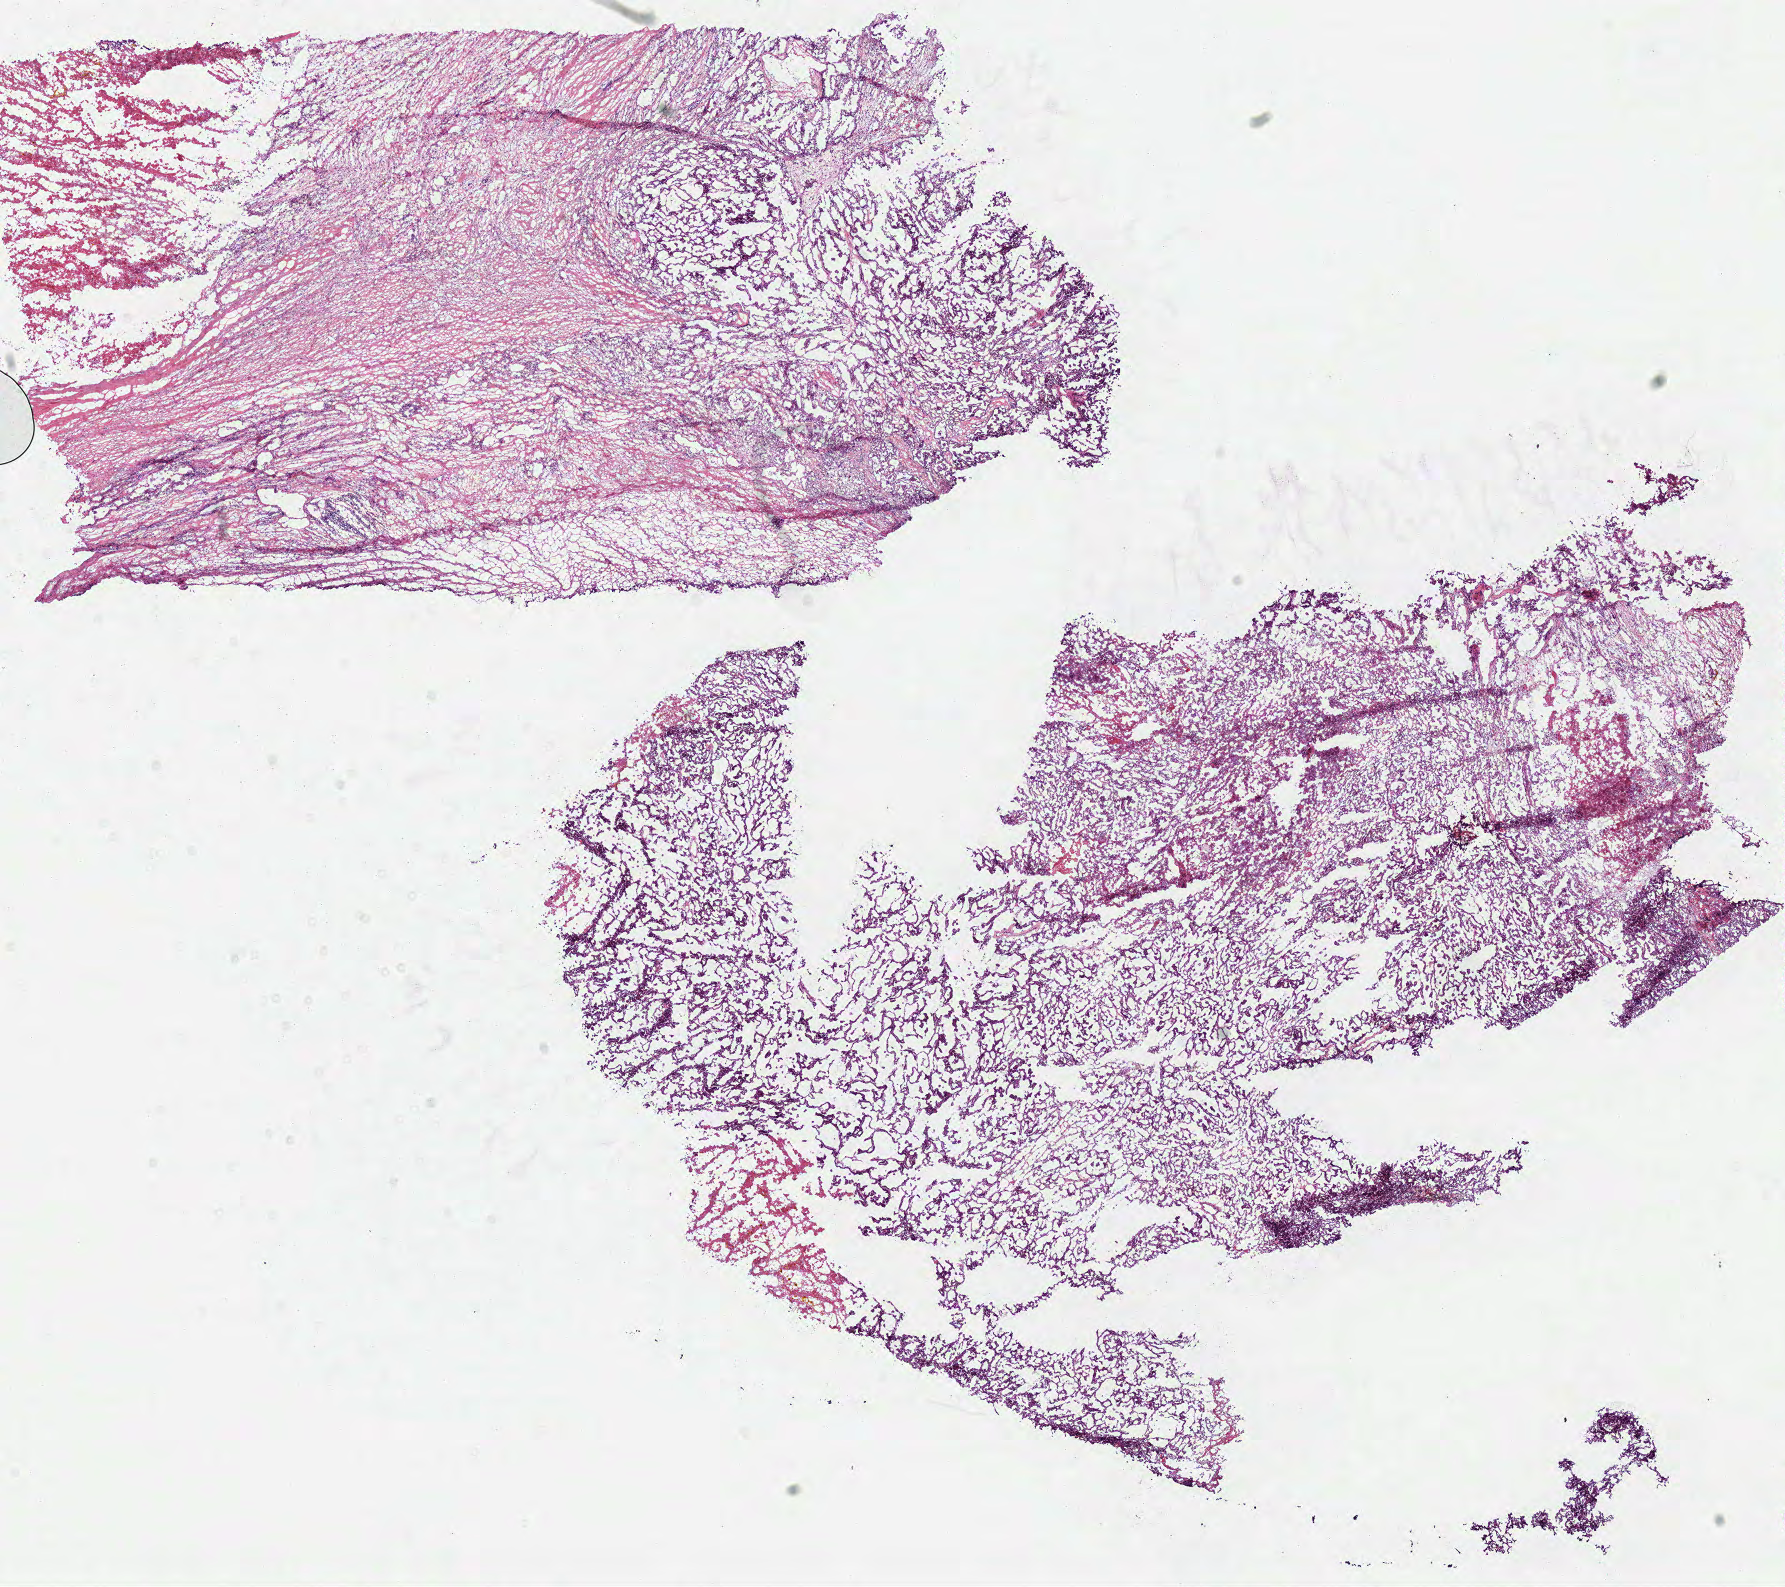
Digitized H&E-stained tissue section (whole slide) — whole scanned area (about 14.1 x 12.5 mm, acquisition: 40x scan) shown as a low-resolution overview; frozen section from the bottom of the tissue portion; kidney, primary tumour sample. Female, age 72 years at initial diagnosis. Slide review estimates, as recorded: tumour cells 52%, tumour nuclei 70%, normal cells 0%, stromal cells 30%, necrosis 18%.
• pathologic diagnosis: Papillary adenocarcinoma, NOS
• TNM: T3 N2 M0
• lymph nodes positive (case pathology): 4 of 14 examined
• AJCC pathologic stage: IV (6th edition)